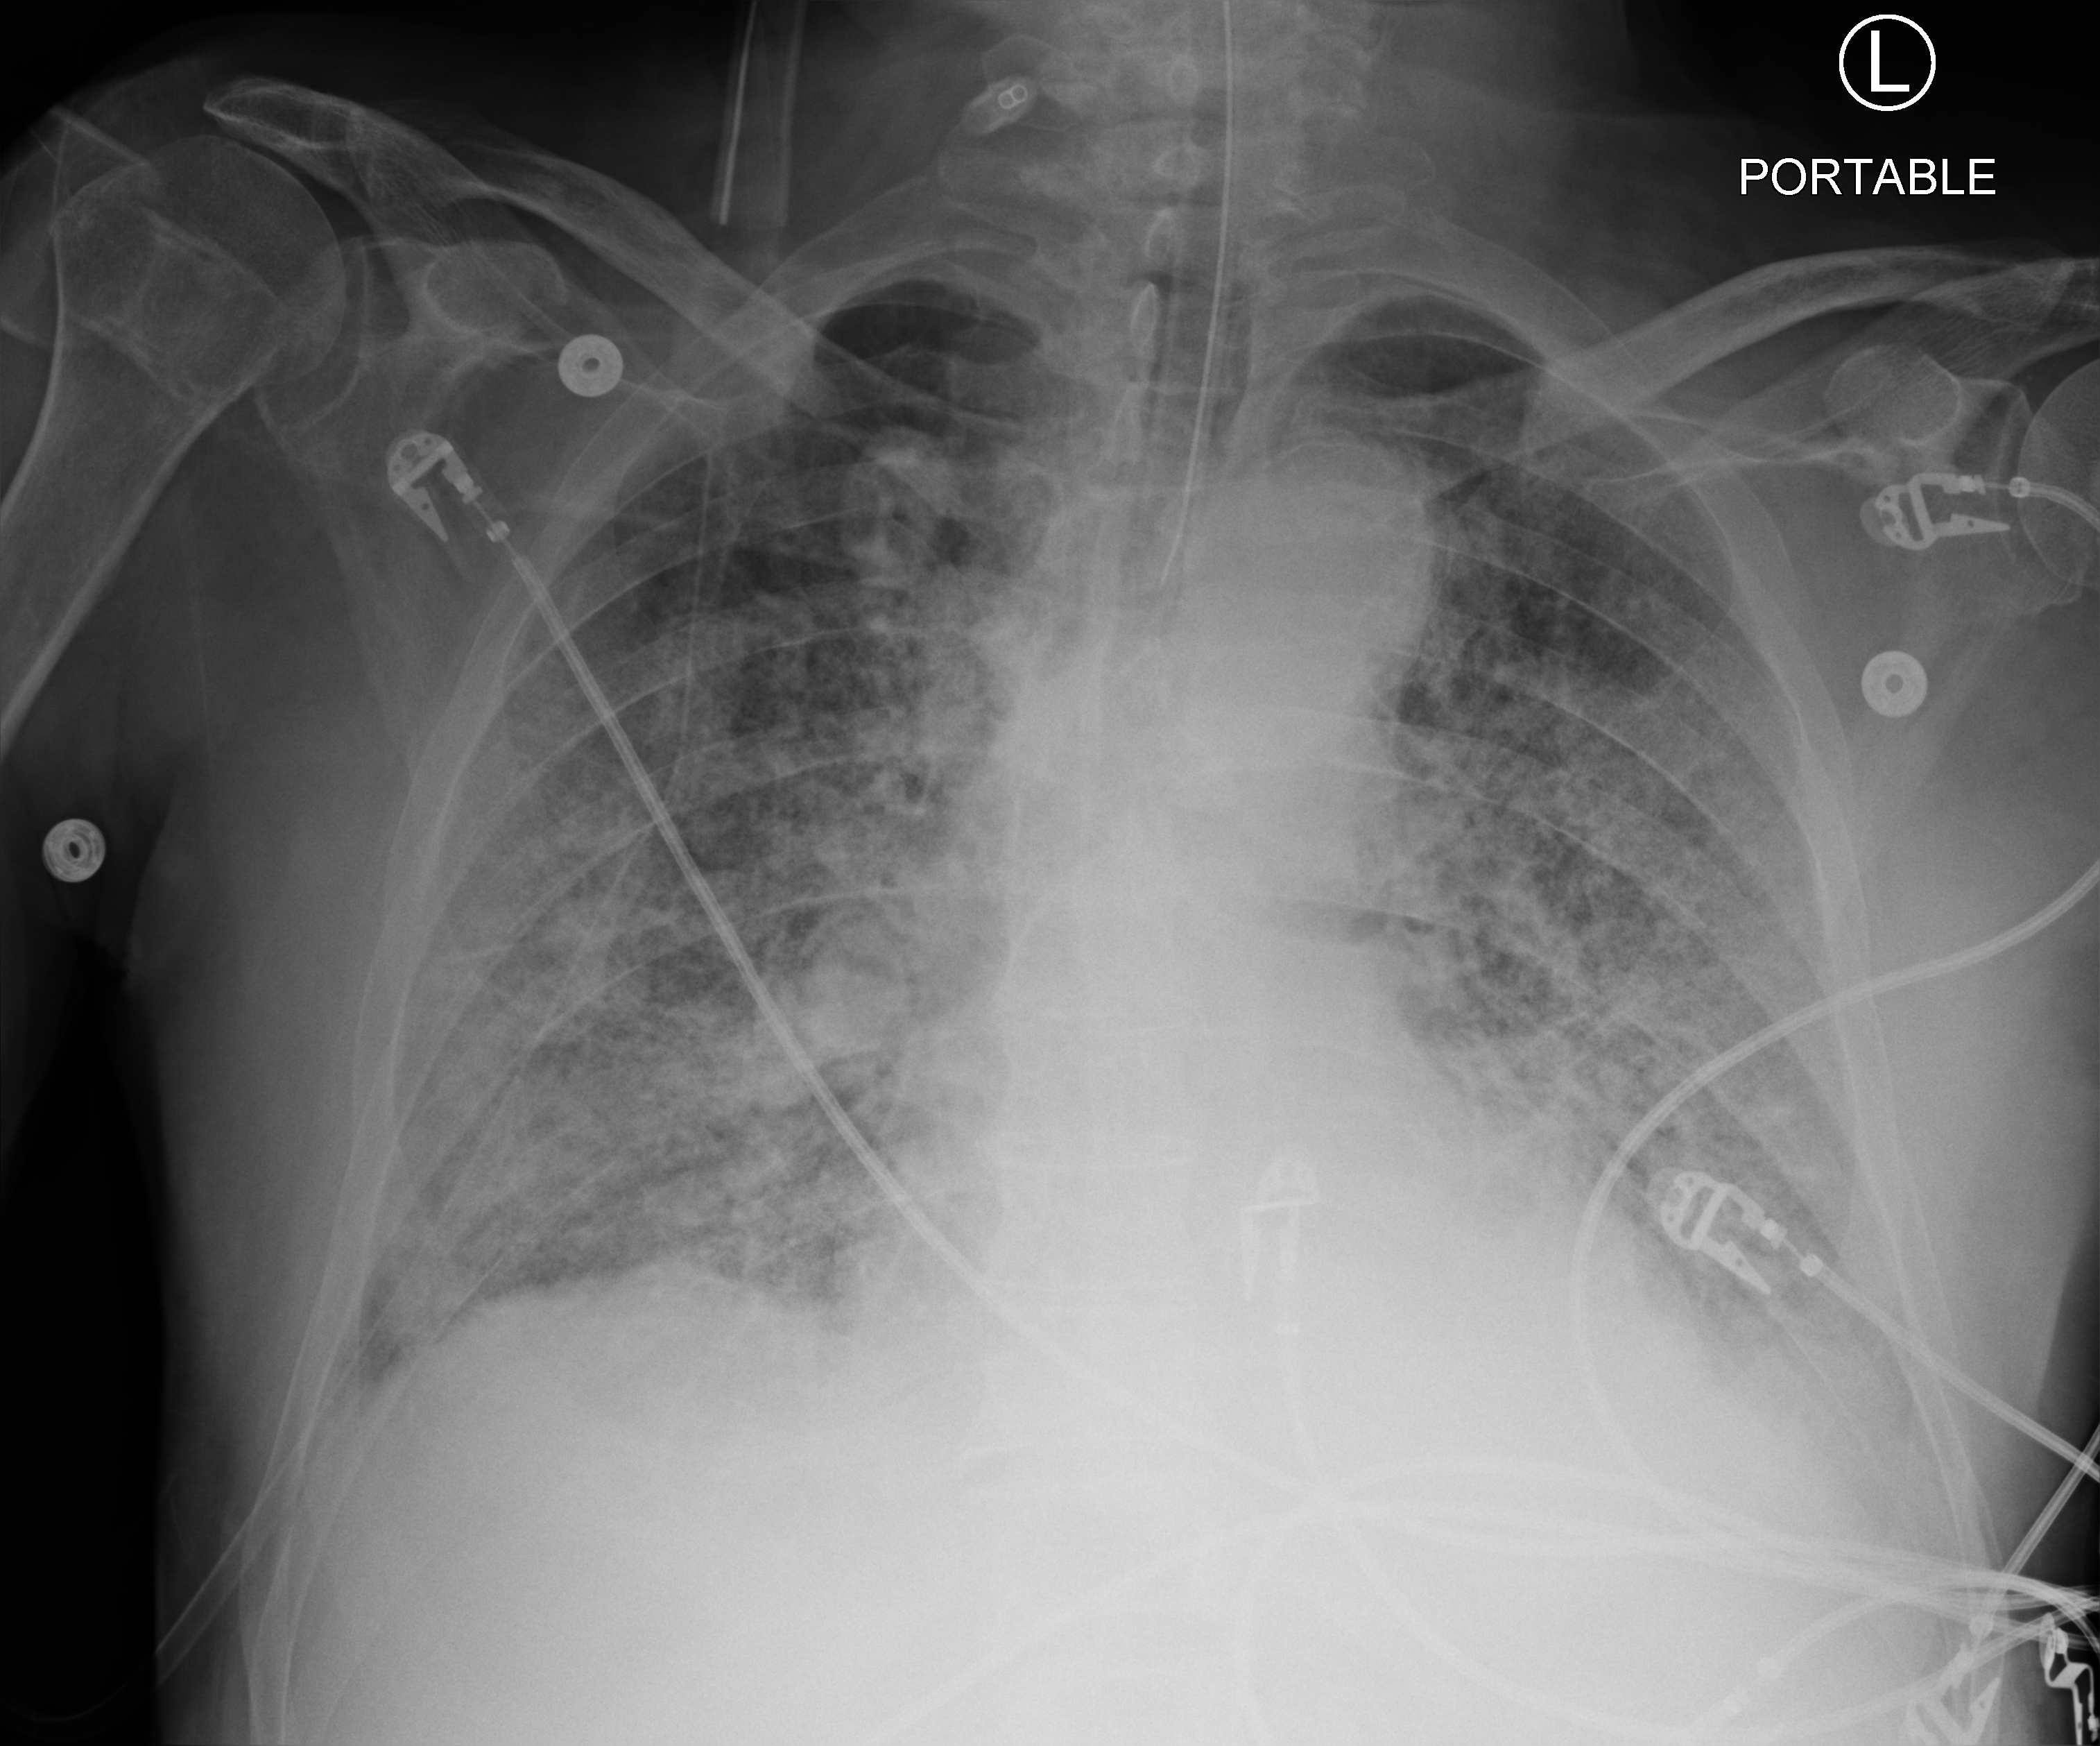
Bedside chest radiograph (computed radiography). Male patient hospitalised with COVID-19, age 75–90 years.
Hospital-stay facts (about this admission, not read from this image; timing relative to this image not recorded):
- hypertension (admission record): no
- admitted to intensive care during this hospital stay: yes
- smoking status (admission record): former